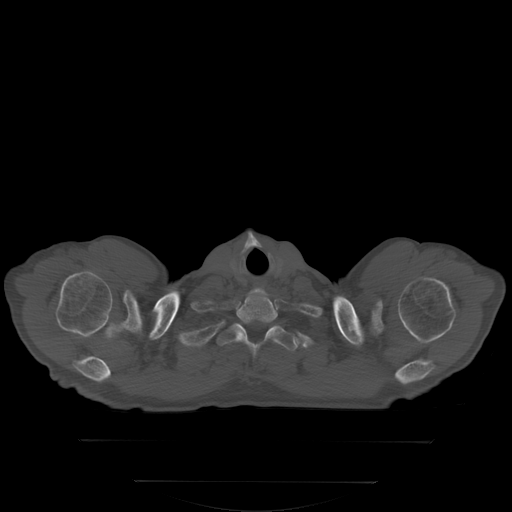
CT including the spine, one axial slice. Slice 292 of 350 in the series (ordered by position). Bone window (W 1800 / L 400 HU). 2.5 mm slice thickness. 512 × 512 image matrix, field of view 500 × 500 mm. Male patient, age 58 years. From the clinical record (not read from this slice): primary cancer: prostate; vertebrae with lytic lesions (as recorded): L1.
Outlined on this slice (semi-automatic segmentation, software-assisted and operator-edited):
- T1 vertebra: bounding box (x1, y1, x2, y2) in pixels: (223, 322, 299, 358)